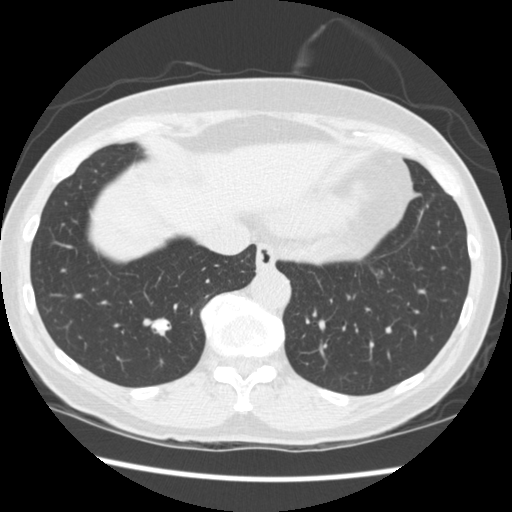
Low-dose screening chest CT, one axial slice; position 68 of 262 along the scan axis; lung window (W 1500 / L -600 HU); 2.5 mm slice thickness; 512 × 512 image matrix, field of view 340 × 340 mm.
Annotated regions visible in this slice (expert manual segmentation):
- lesion 1 (tumor, lower lobe of right lung): bounding box [x1, y1, x2, y2] px = [152, 319, 171, 336]